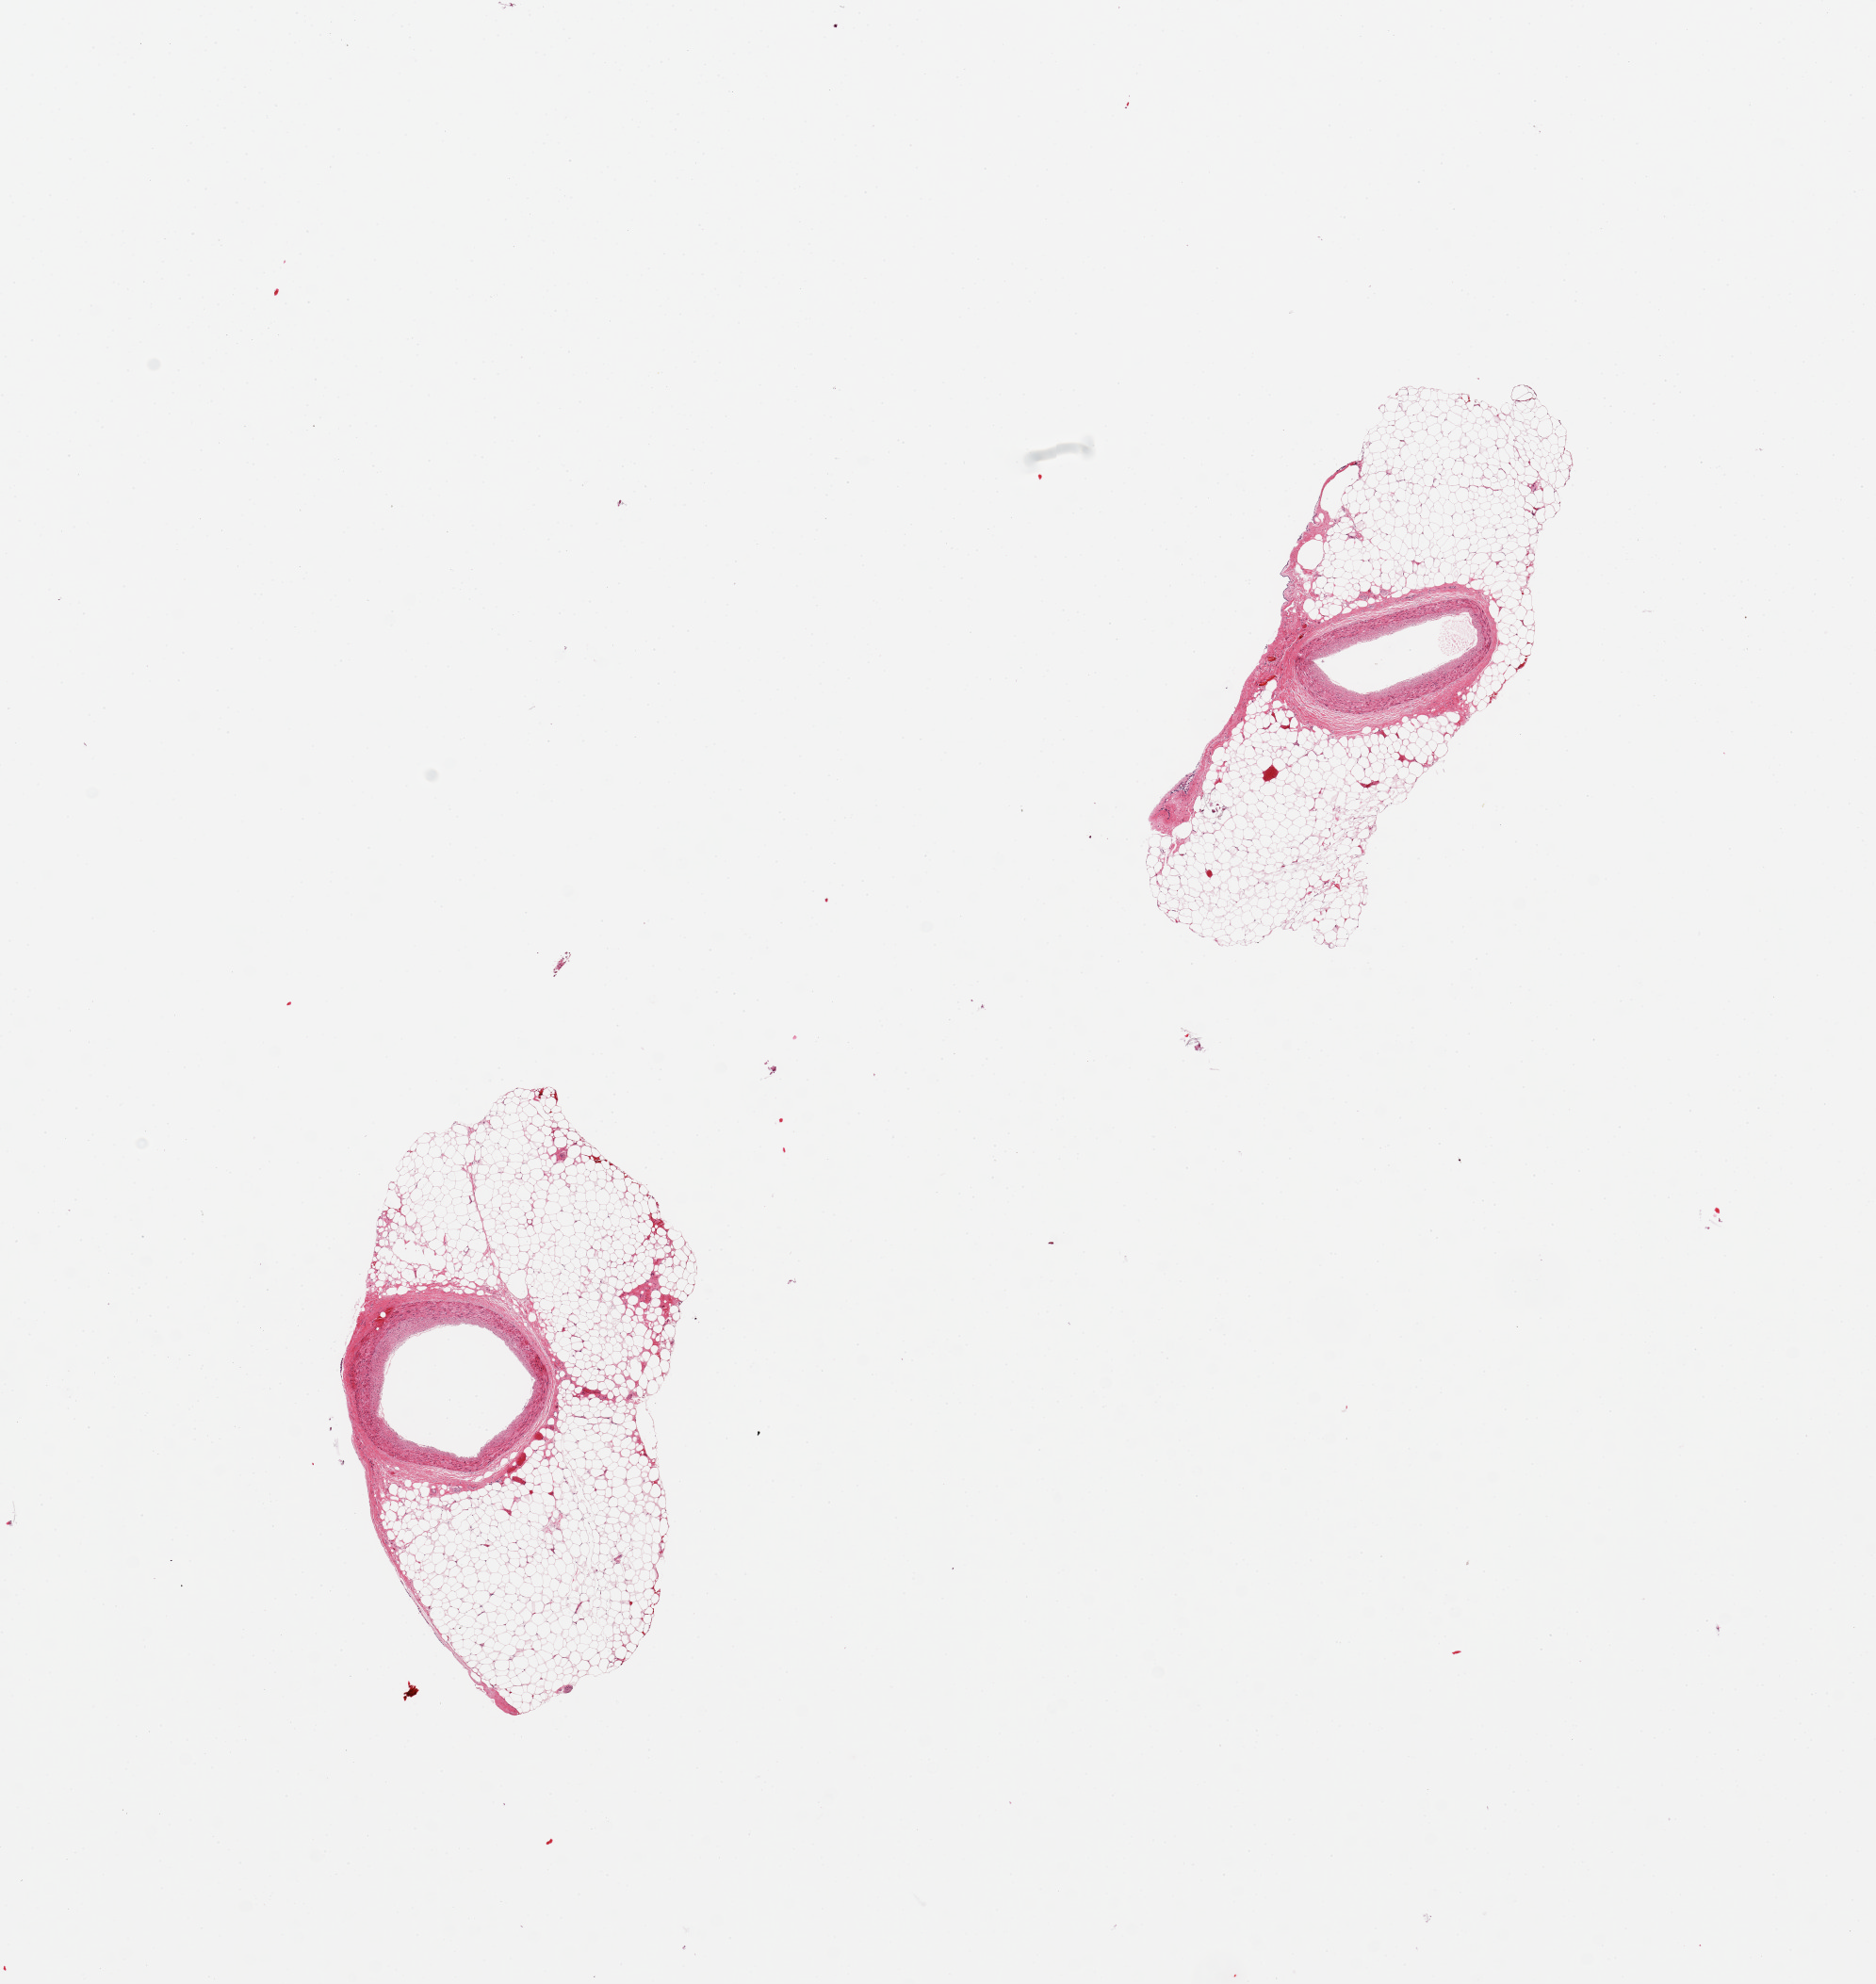
Digitized haematoxylin and eosin-stained section, low-resolution overview of the scanned area, about 15.8 x 16.7 mm (acquisition: 20x scan); PAXgene-fixed paraffin-embedded (PFPE) section; section of coronary artery (target tissue); tissue donor sample. Donor: female.
Reviewer comment on this tissue sample: 2 pieces, rims of adherent fat on both up to ~2.mm.